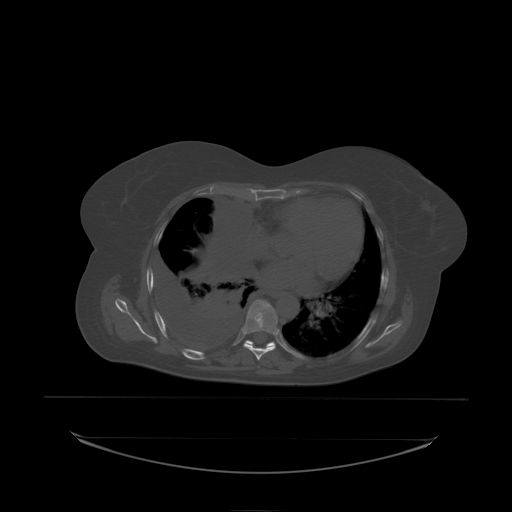
CT including the spine, one axial slice. Position 139 of 242 along the scan axis. Bone window (W 1800 / L 400 HU). 2.5 mm slice thickness. 512 × 512 image matrix, field of view 500 × 500 mm. Female patient, age 53 years. From the clinical record (not read from this slice): primary cancer: lung; vertebrae with lytic lesions (as recorded): T7, L1.
Annotated regions visible in this slice (semi-automatically segmented with operator editing):
- T7 vertebra: bounding box [x1, y1, x2, y2] px = [244, 300, 278, 335]